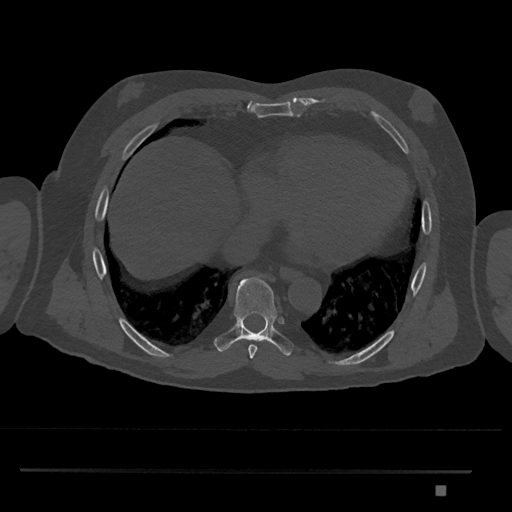
CT including the spine, one axial slice. Position 1120 of 1134 along the scan axis. Bone window (W 1800 / L 400 HU). 0.5 mm slice thickness. 512 × 512 image matrix. Male patient, age 65 years. From the clinical record (not read from this slice): primary cancer: prostate.
Outlined on this slice (semi-automatically segmented with operator editing):
- T8 vertebra: bounding box [x1, y1, x2, y2] px = [214, 275, 294, 356]